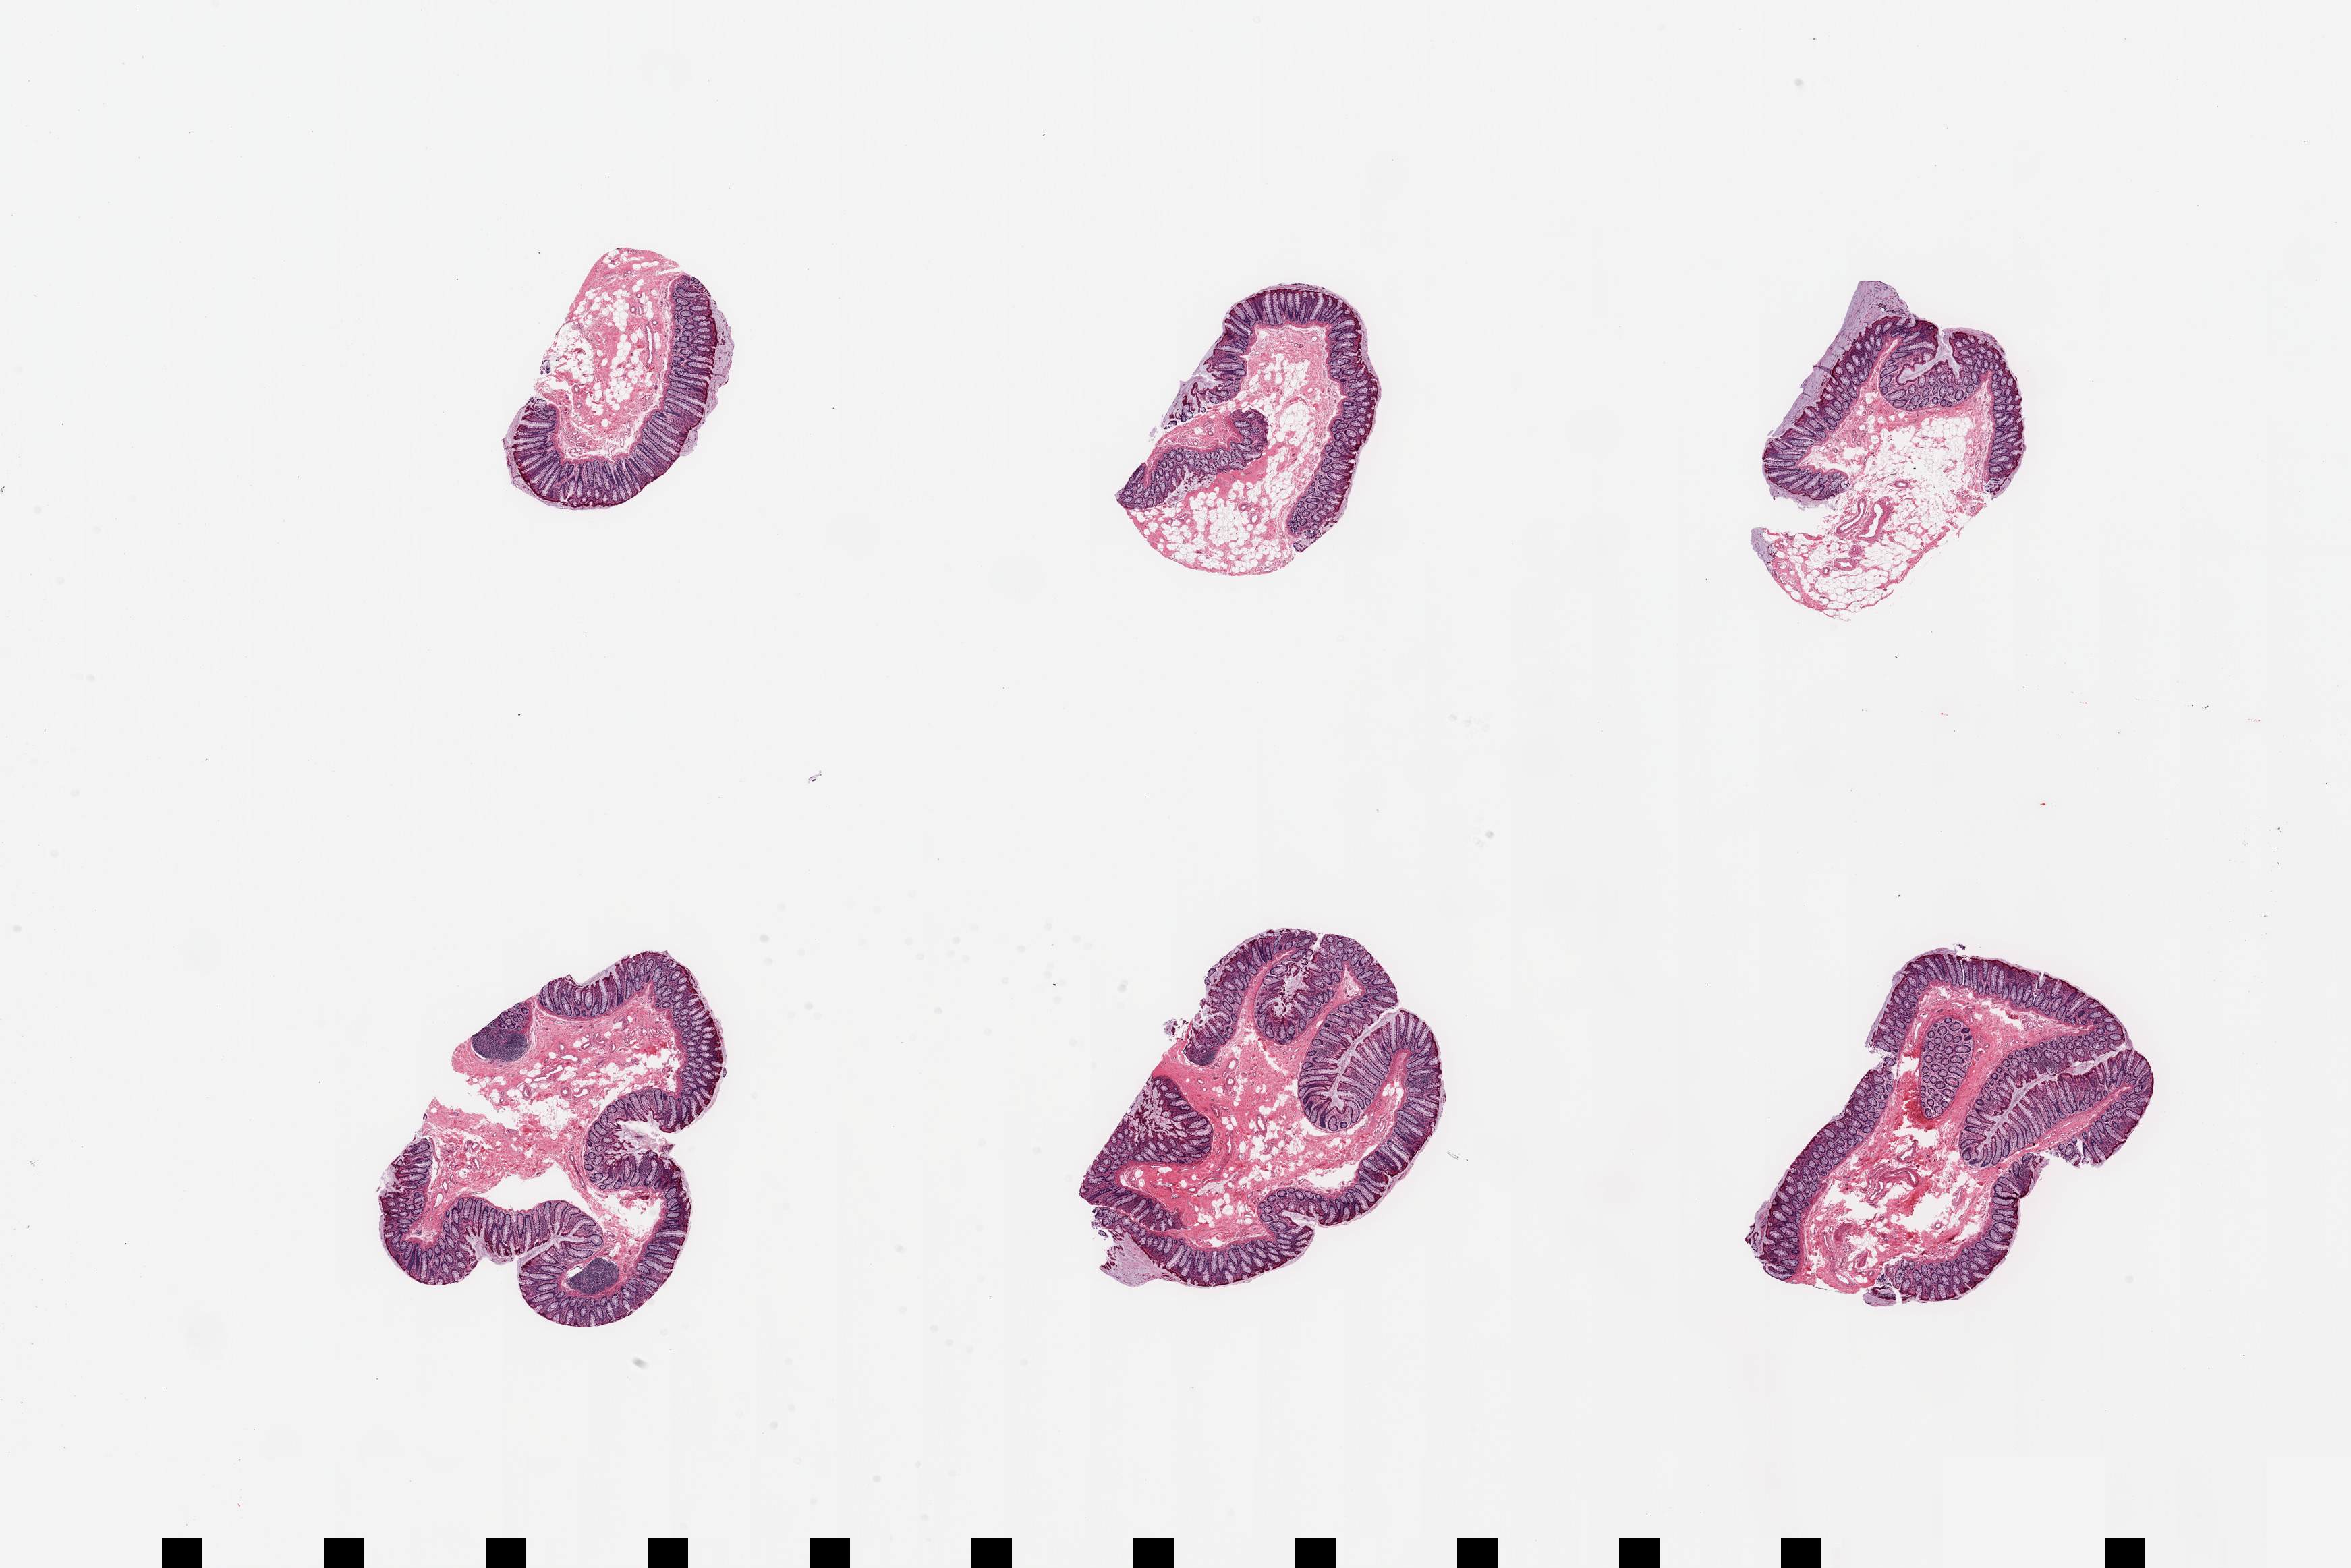
Whole-slide image, hematoxylin and eosin (H&E) stain — a low-resolution overview of the entire scanned area, about 27.6 x 18.4 mm; PAXgene-fixed paraffin-embedded (PFPE) section; sampled site (target tissue): ileum; donor tissue sample.
• pathologist's review note for this sample: 6 pieces, not ileum, colonic mucosa, unknown origin